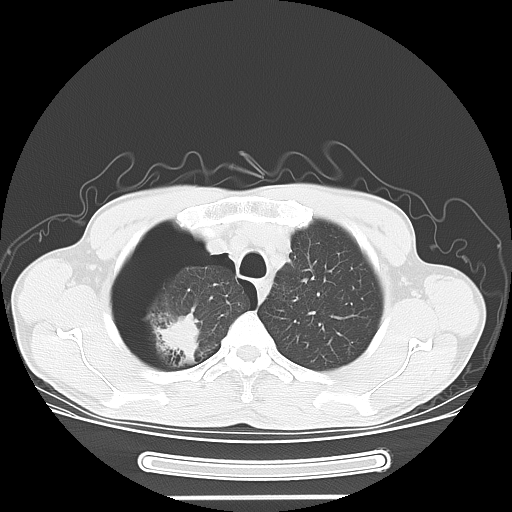
Chest CT, one axial slice. Slice 55 of 67 in the series (ordered by position). Lung window (W 1500 / L -600 HU). 5 mm slice thickness. 512 × 512 image matrix. Male patient. Case-level facts recorded for this patient, not image findings: clinical TNM (as recorded): T1c N0 M0.
Structures marked on this image (rectangle marked by the reading radiologist):
- lung tumour (recorded histology: adenocarcinoma): bounding box <155,310,202,373> (left, top, right, bottom; pixels)